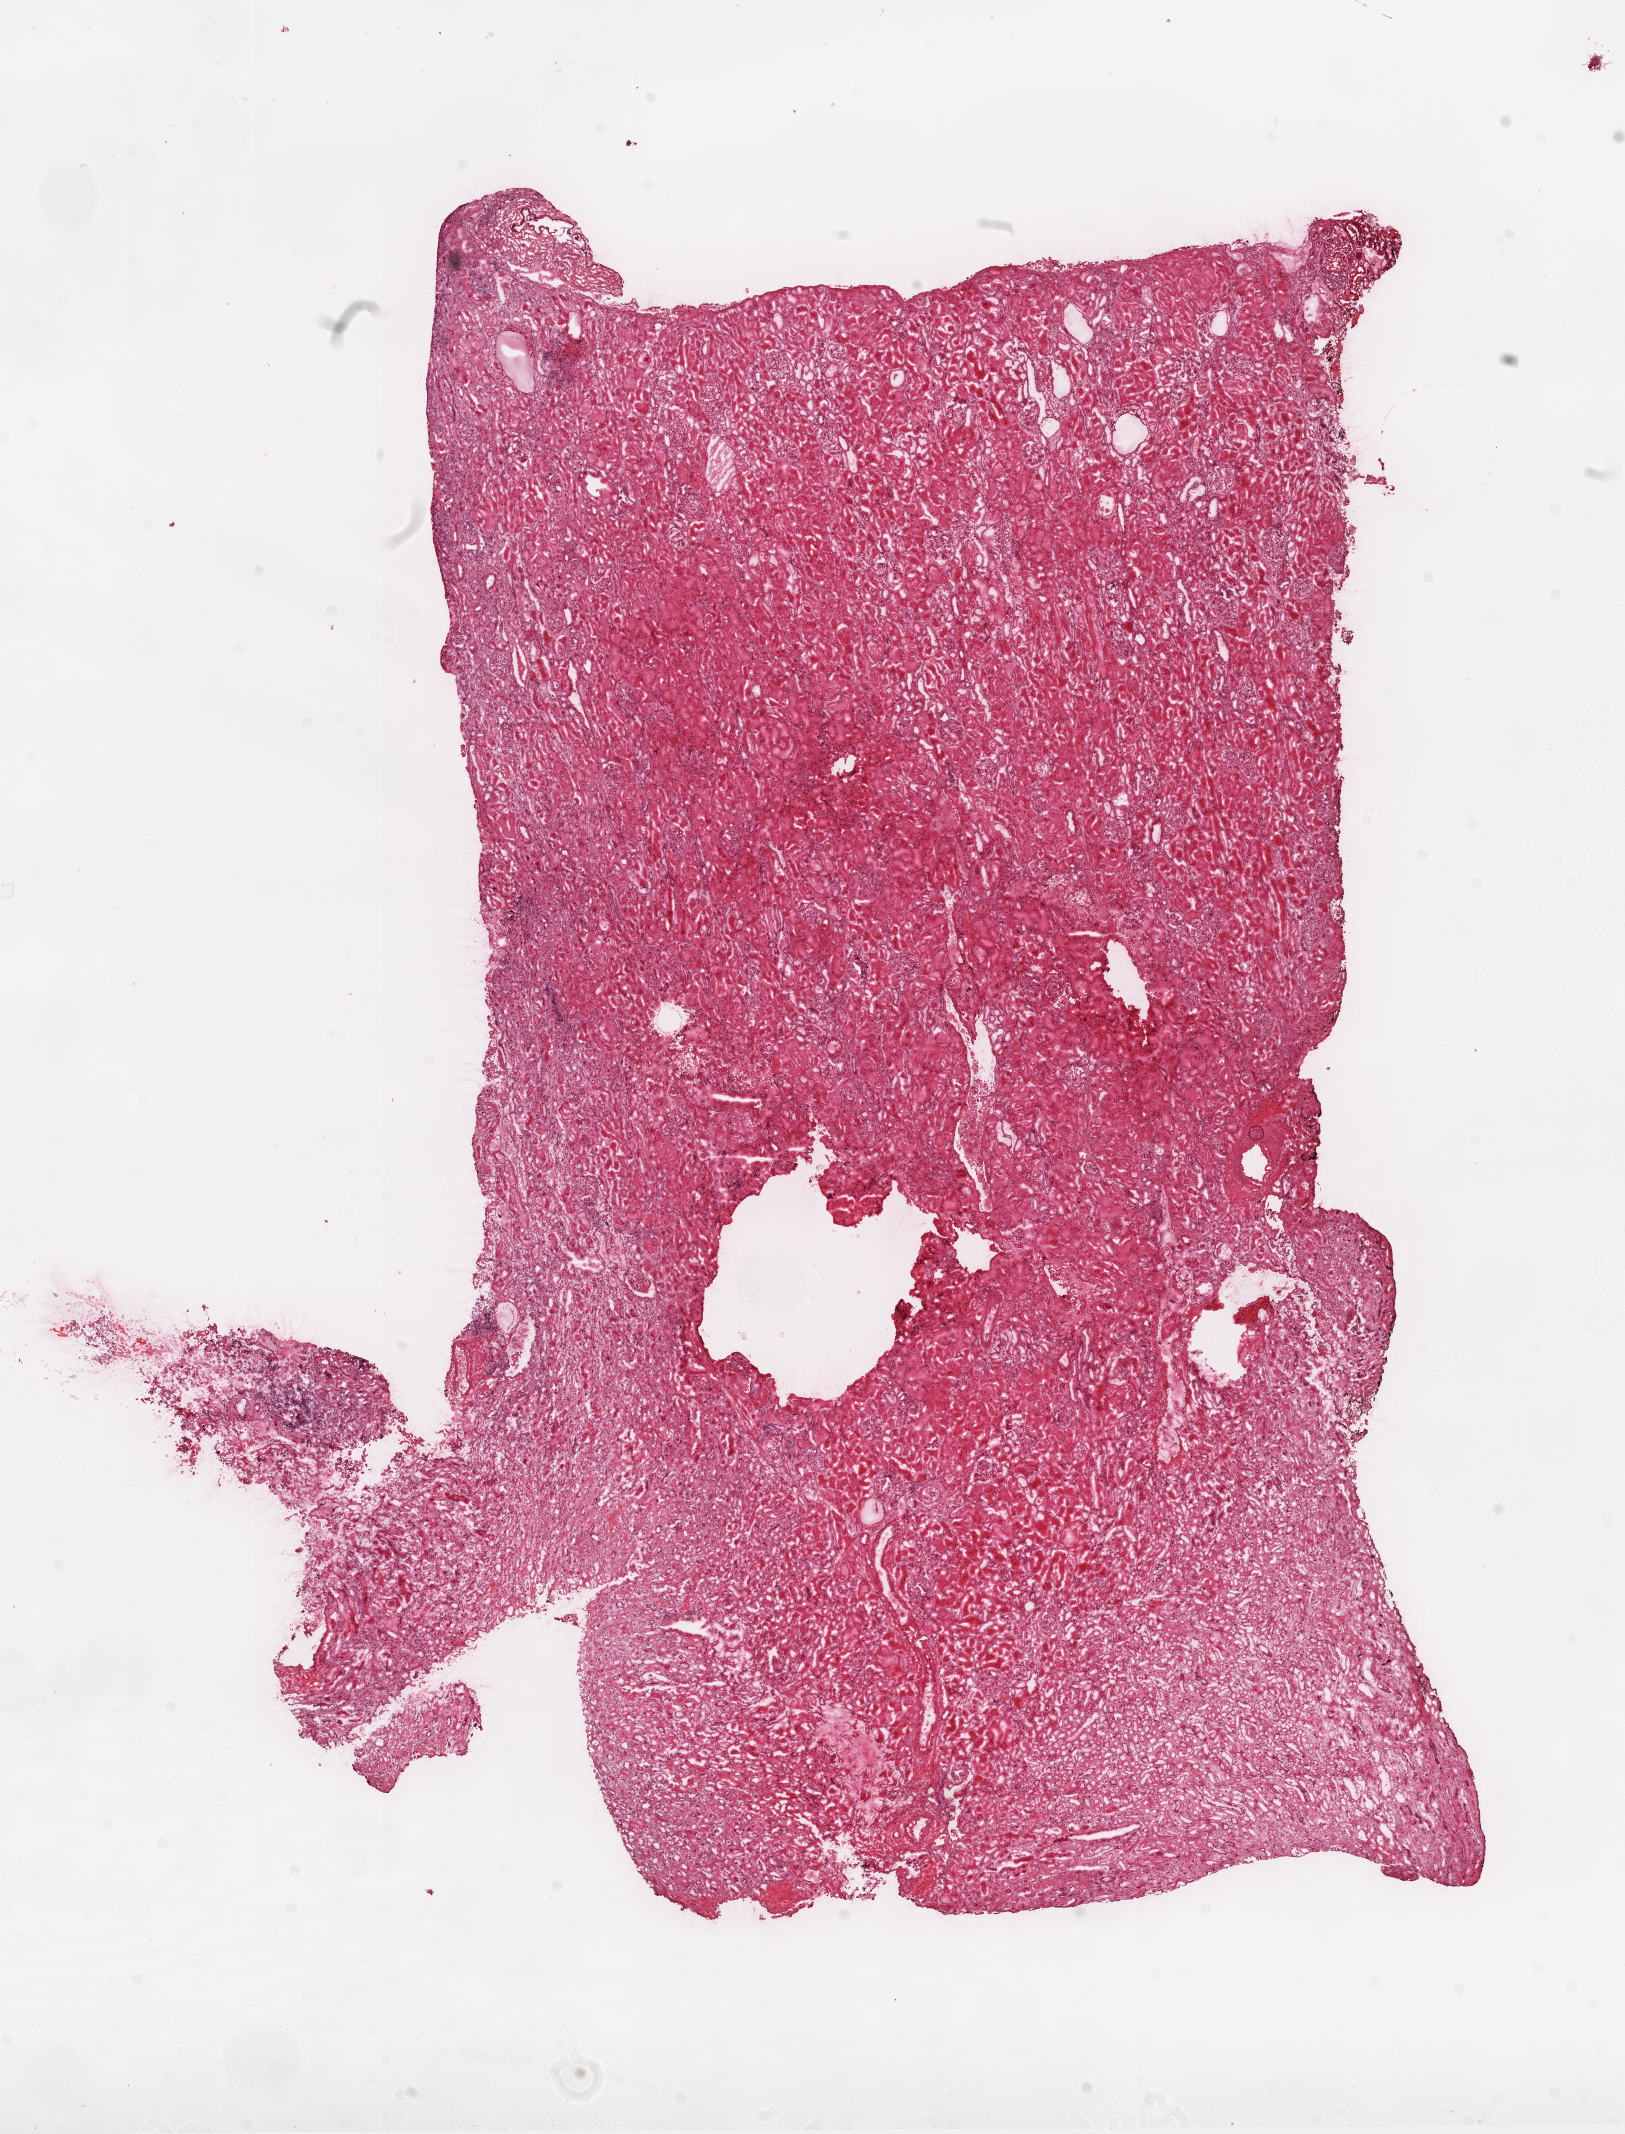
Whole-slide histology image, H&E — whole scanned area (about 13.0 x 17.1 mm) shown as a low-resolution overview. Frozen section. Sample: solid tissue normal (non-tumour tissue), kidney. Male, age 59 years at initial diagnosis.
This section: solid tissue normal sample (biorepository sample class). Patient diagnosis: Clear cell adenocarcinoma, NOS.